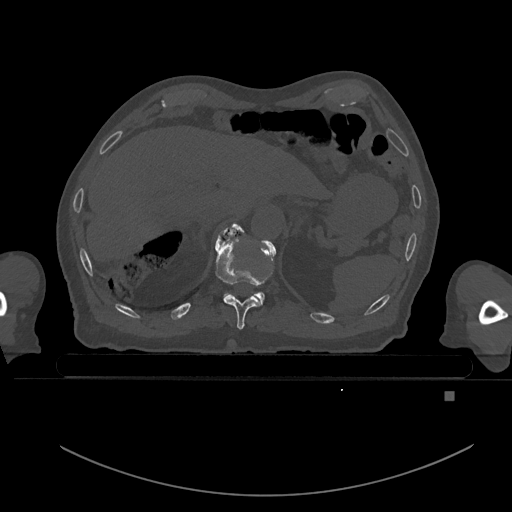
CT including the spine, one axial slice; slice 69 of 969 in the series (ordered by position); bone window (W 1800 / L 400 HU); 512 × 512 image matrix, field of view 456 × 456 mm. Male patient, age 82 years. From the clinical record (not read from this slice): primary cancer: prostate.
Outlined on this slice (semi-automatically segmented with operator editing):
- T10 vertebra: bounding box <215,224,266,330> (left, top, right, bottom; pixels)
- T11 vertebra: <219,224,273,304>